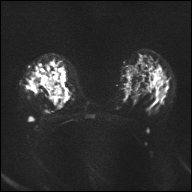
Breast MRI, one axial slice; slice 26 of 32 in the series (ordered by position); diffusion-weighted series; image 2 of 4 stored at this slice position (different b-values; order by instance number); 1.5 T; 4 mm slice thickness; 192 × 192 image matrix, field of view 360 × 360 mm. Female patient.
Outlined on this slice (manually delineated by an expert):
- tumour on diffusion-weighted imaging: bounding box [x1, y1, x2, y2] px = [43, 70, 67, 96]